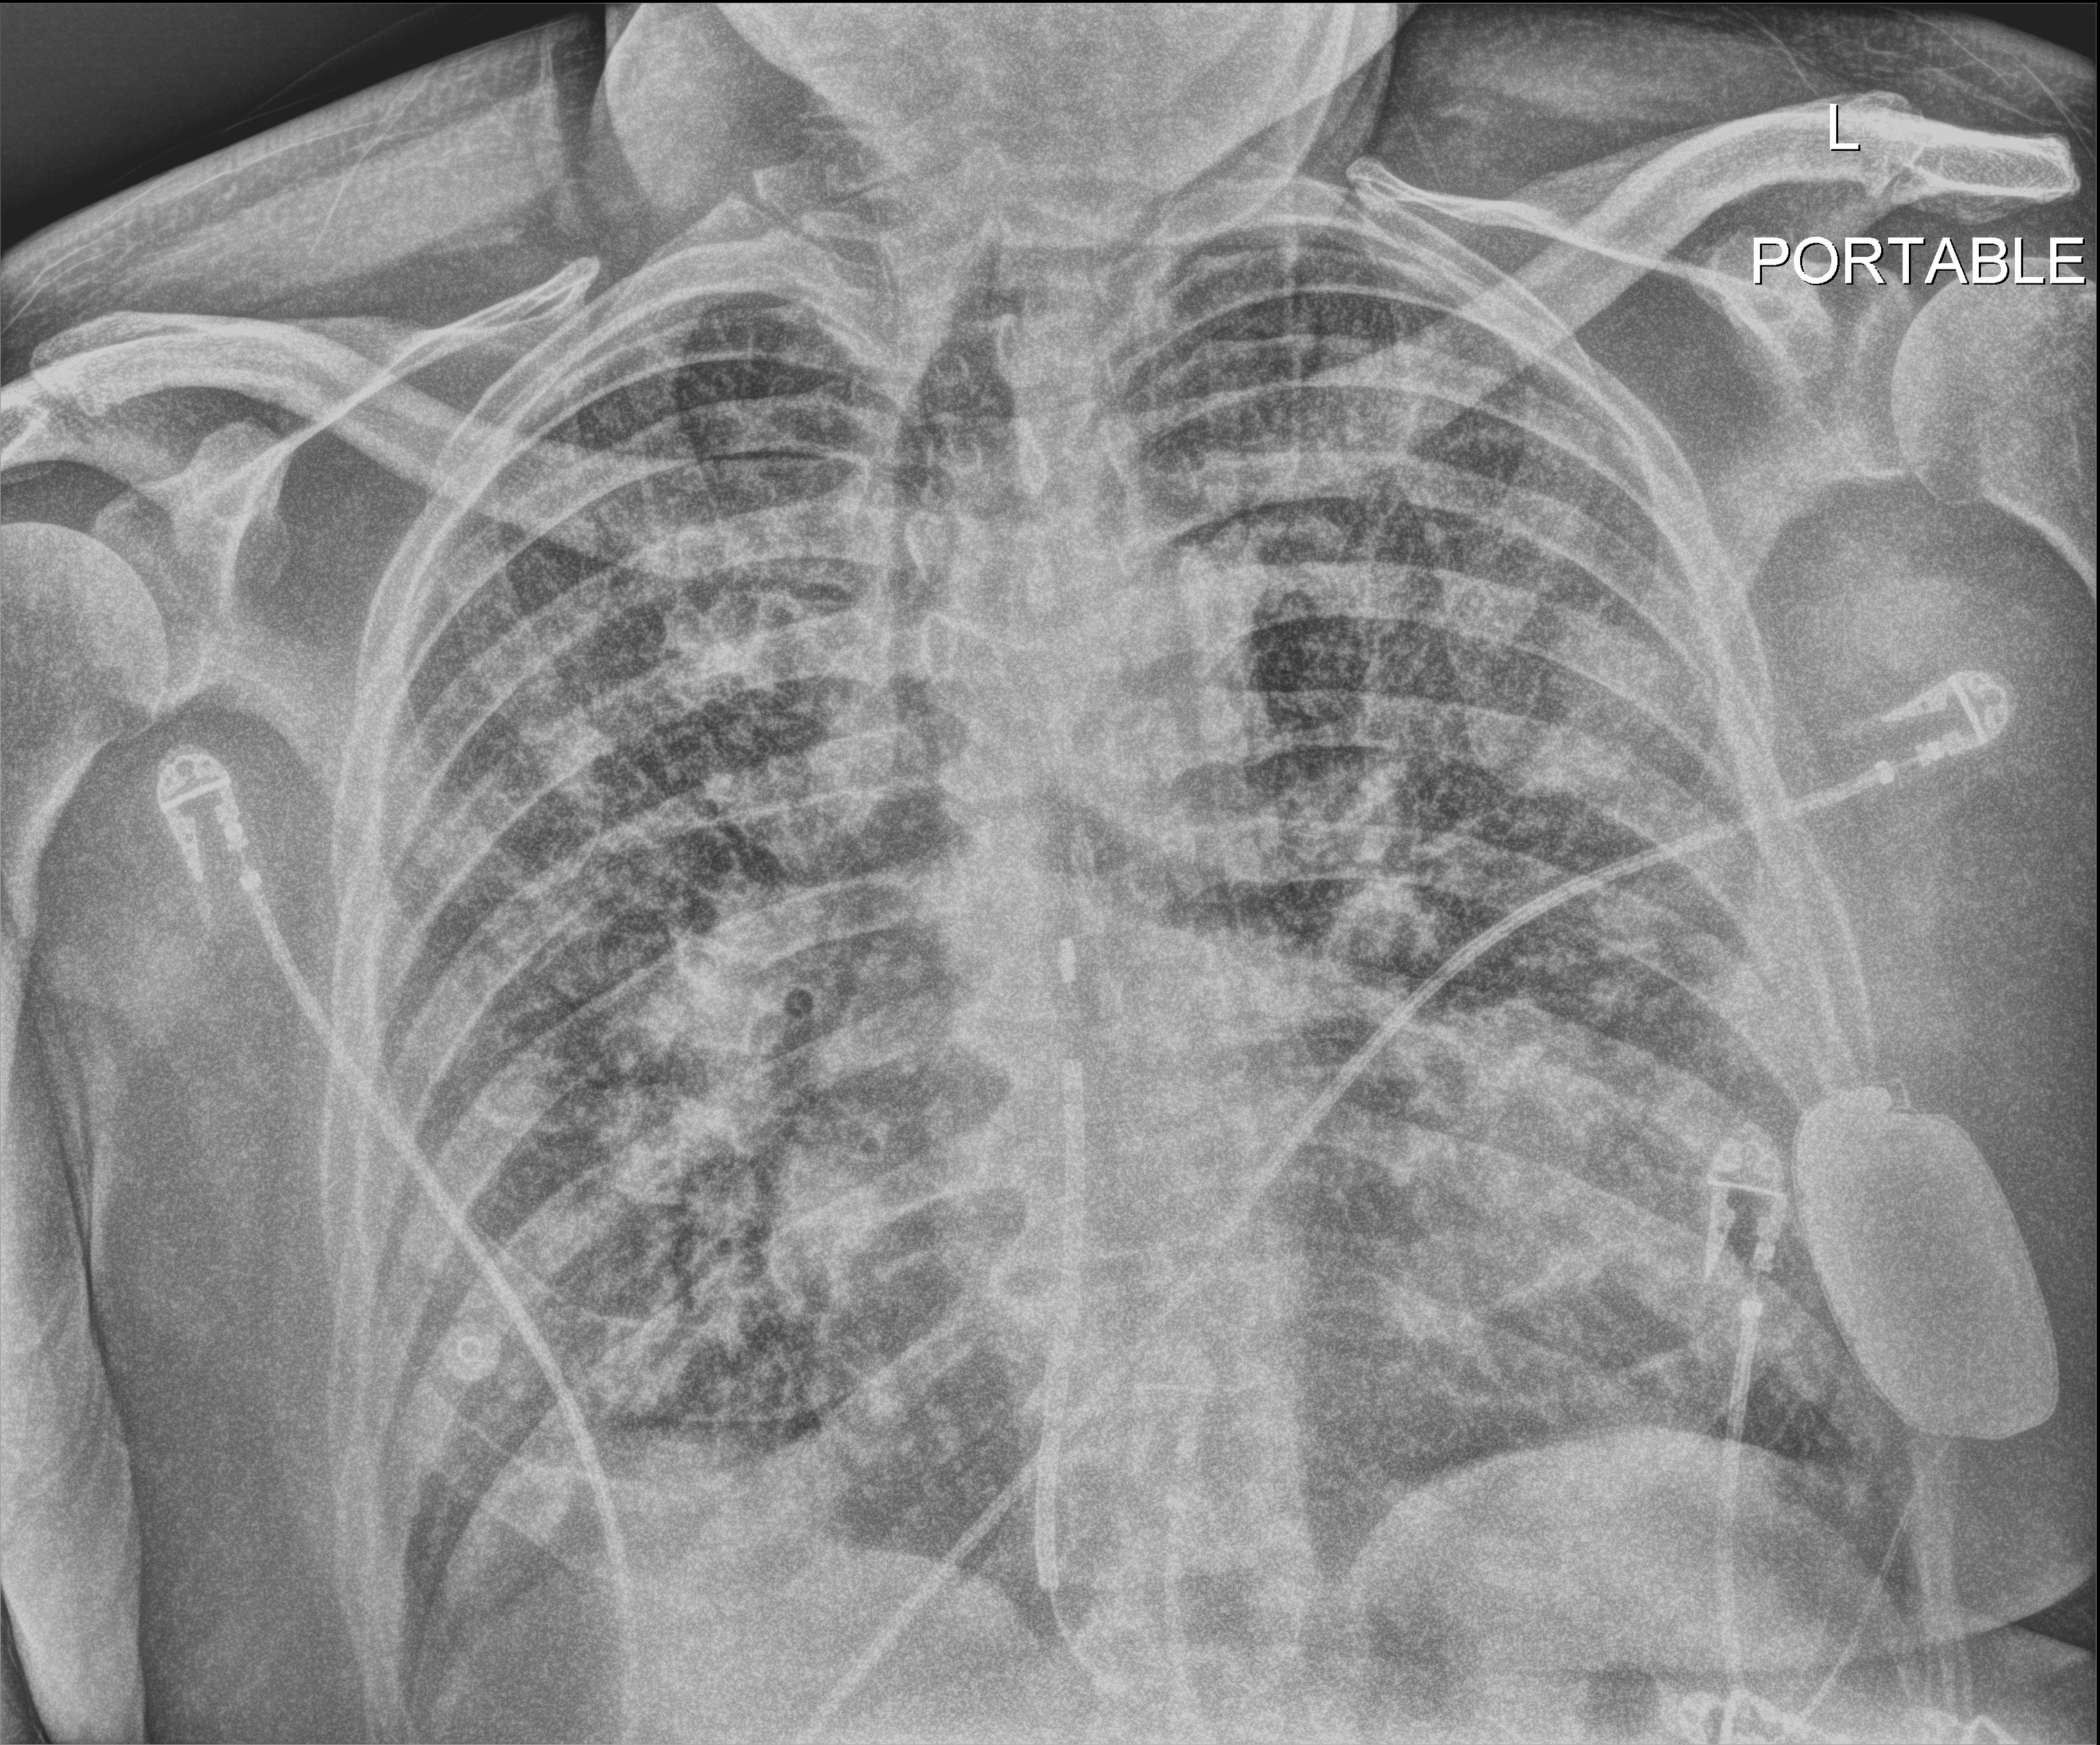
Bedside chest radiograph (digital radiography). Male patient hospitalised with COVID-19, age 60–74 years.
Hospital-stay facts (about this admission, not read from this image; timing relative to this image not recorded): admitted to intensive care during this hospital stay: yes.